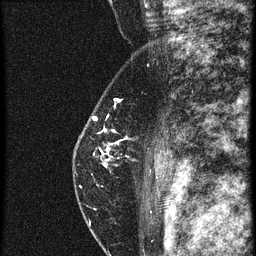
Breast MRI (dynamic contrast-enhanced), one sagittal slice; slice 41 of 60 in the series (ordered by position); 4 images stored at this slice position (order not interpretable as contrast timing); 1.5 T; TE 4.2 ms, TR 20.4 ms; 1.5 mm slice thickness; 256 × 256 image matrix, field of view 180 × 180 mm. Patient: female, 46 years. From the clinical record (not read from this slice): setting: breast cancer imaged before/during neoadjuvant chemotherapy; receptor status: triple-negative.
Structures marked on this image (semi-automatically segmented with operator editing):
- analysis volume of interest (the breast-tissue region the enhancement analysis was run in; not a lesion): bounding box (x1, y1, x2, y2) in pixels: (72, 82, 158, 201)
- tumour enhancement mask (voxels above the 90 % enhancement threshold inside the analysis volume of interest): (102, 116, 111, 165)